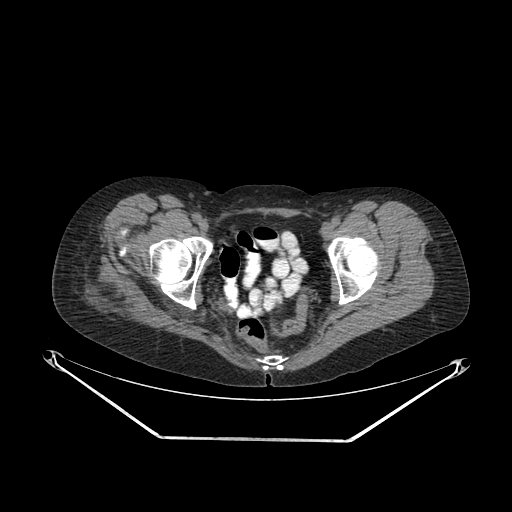
CT of an extremity soft-tissue mass (from a PET/CT study), one axial slice; slice 52 of 267 in the series (ordered by position); soft-tissue window (W 400 / L 40 HU); 512 × 512 image matrix, field of view 500 × 500 mm. Female patient. Case-level facts recorded for this patient, not image findings: histological type: epithelioid sarcoma with vascular differentiation; site of the primary tumour: right buttock.
Annotated regions visible in this slice (expert contour drawn on MRI and transferred to this co-registered scan by the dataset authors):
- gross tumour volume (mass): bounding box (x1, y1, x2, y2) in pixels: (75, 267, 140, 318)